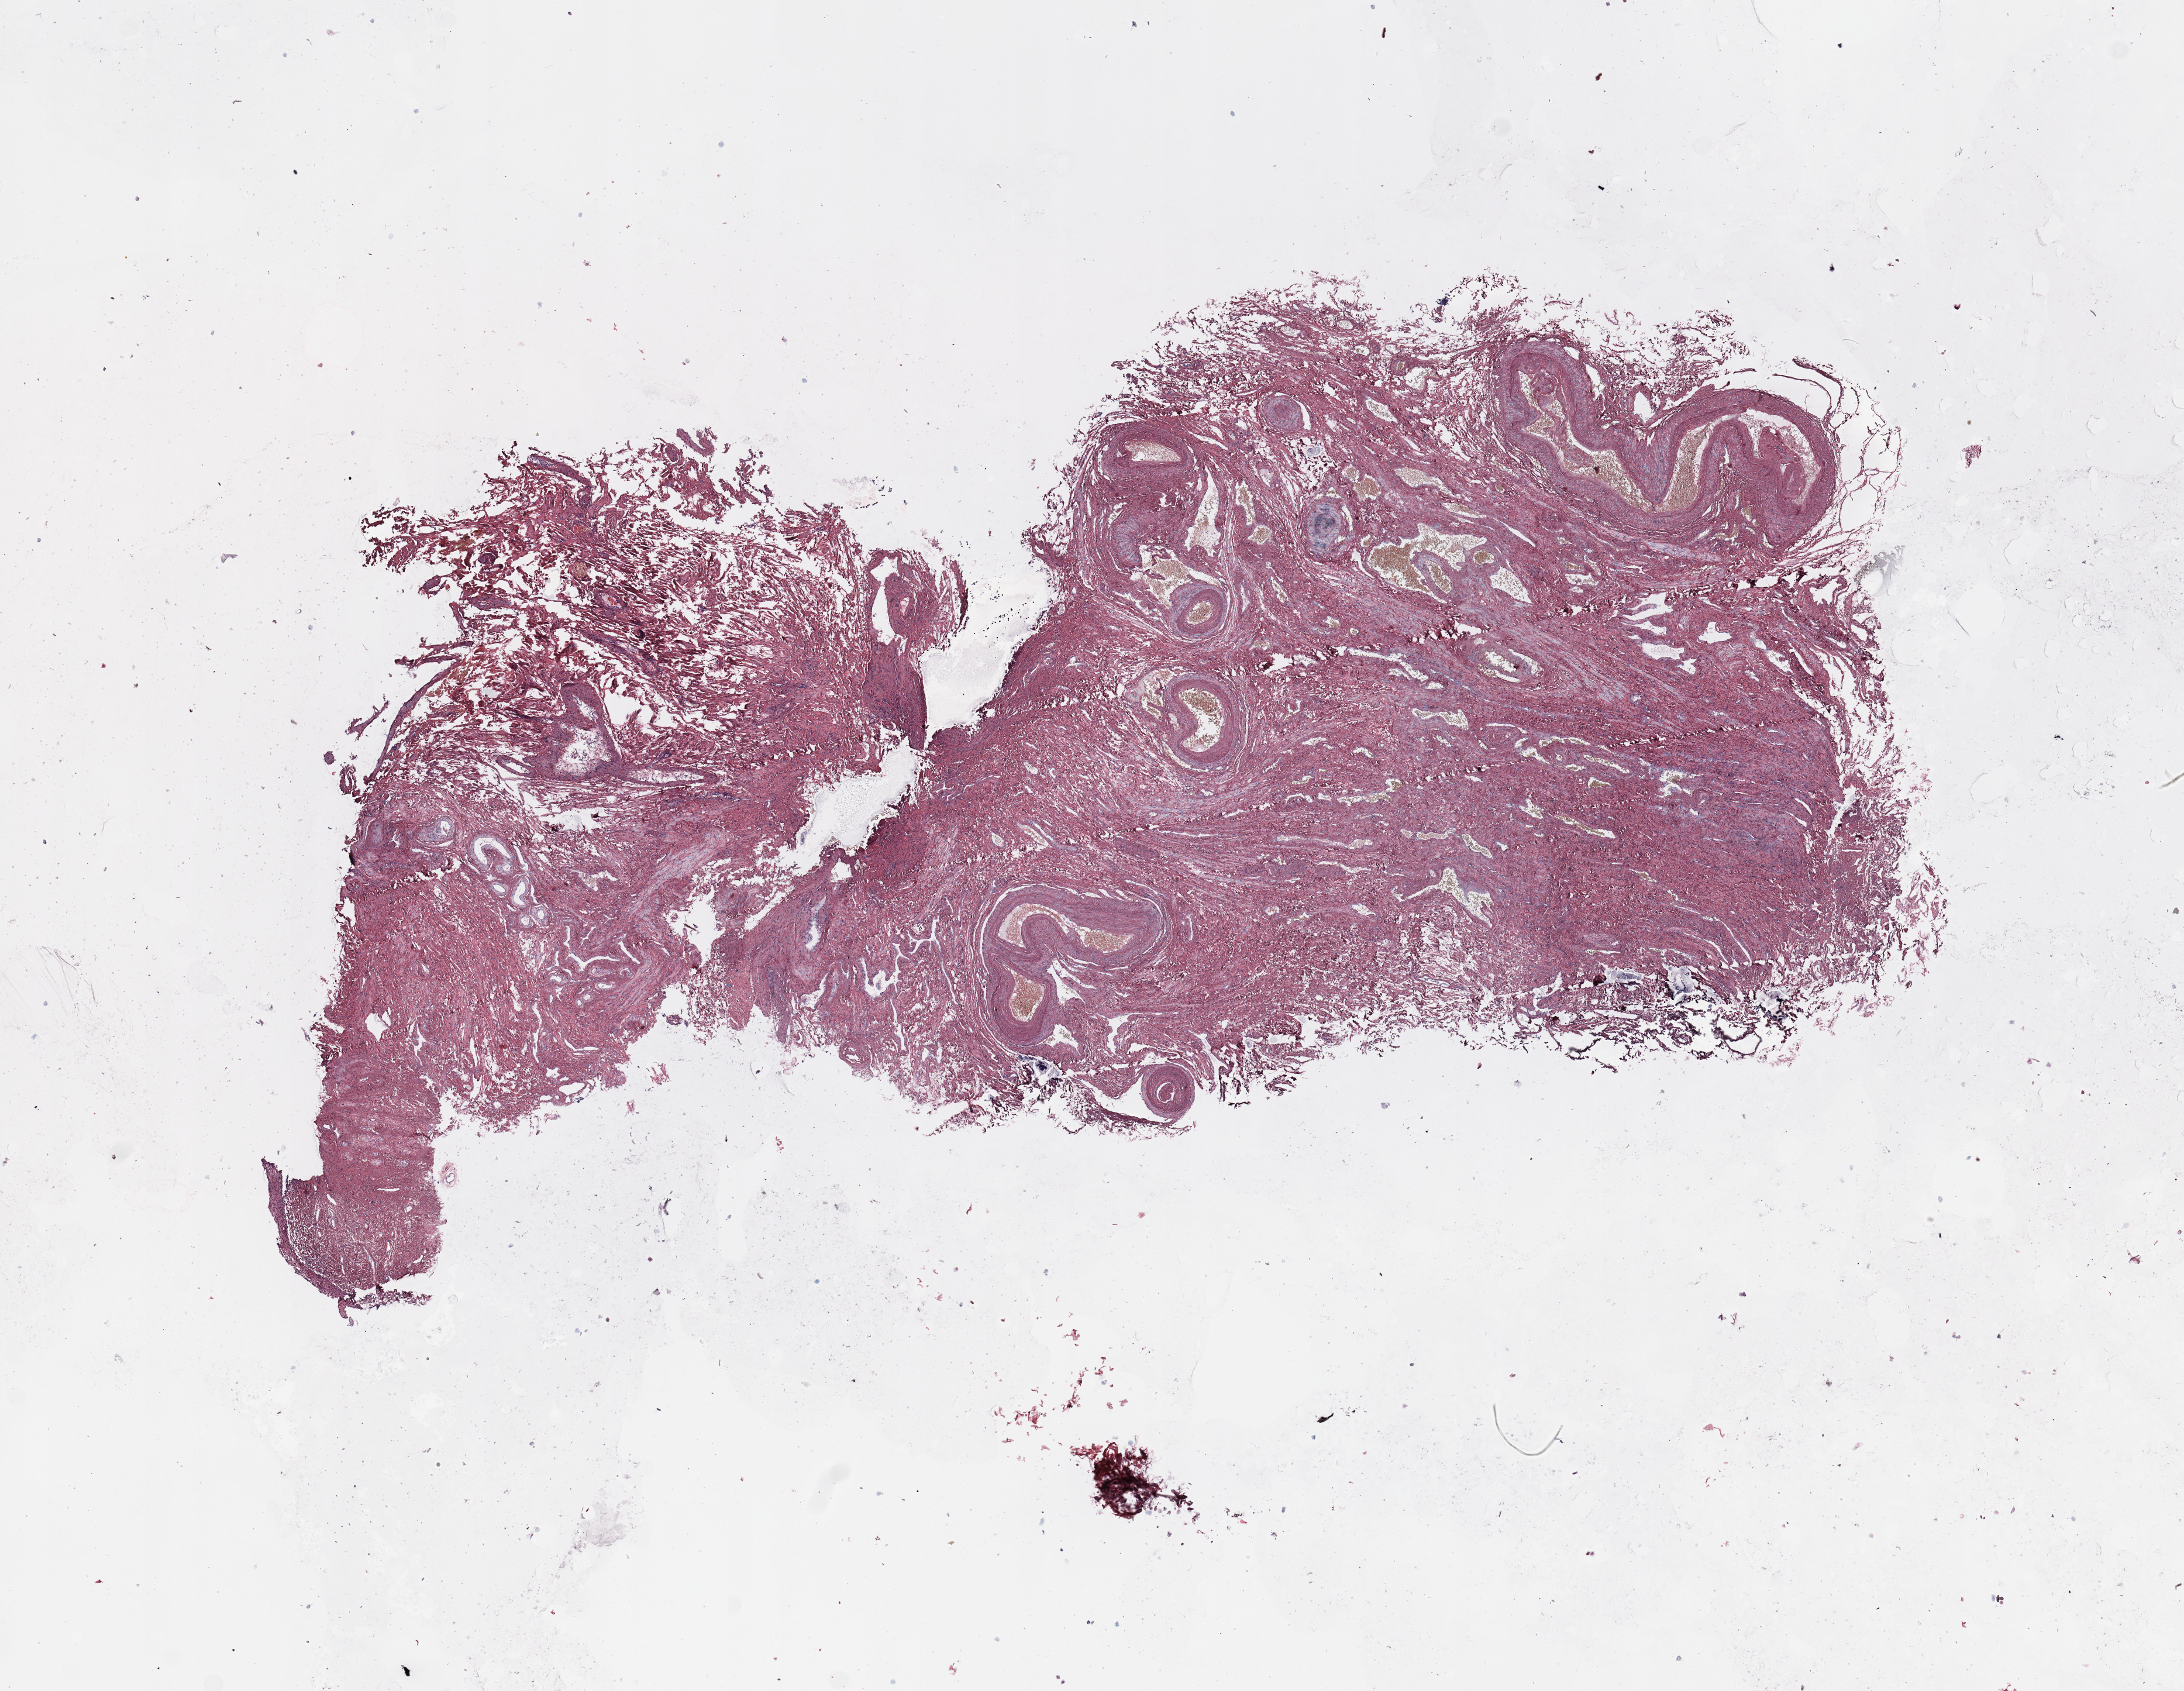
H&E whole-slide image, whole scanned area (about 14.8 x 11.4 mm) shown as a low-resolution overview; uterus, normal (non-tumour) tissue. 63-year-old female patient.
• this section: normal (non-tumour) tissue from the same patient
• patient diagnosis: Endometrioid adenocarcinoma, NOS